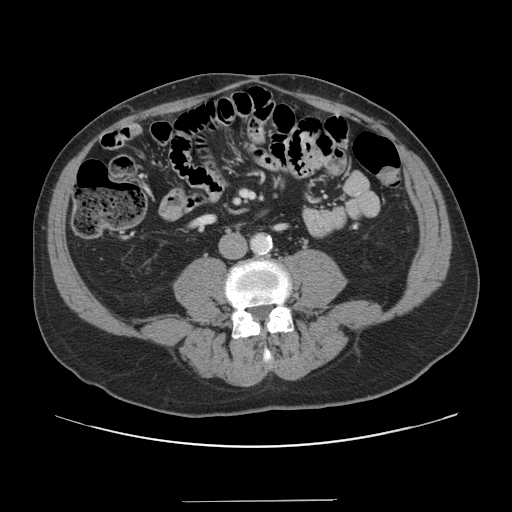
Contrast-enhanced abdominal CT, one axial slice. Slice 13 of 151 in the series (ordered by position). 120 kVp. Intravenous contrast given. Soft-tissue window (W 400 / L 40 HU). 2.5 mm slice thickness. 512 × 512 image matrix. Male patient, age 63 years. From the clinical record (not read from this slice): diagnosis: colorectal cancer liver metastases, imaged before liver resection; multiple liver metastases: no; largest metastasis: 2.1 cm; chemotherapy before resection: no.
Structures marked on this image (manually delineated by an expert):
- portal vein (with intrahepatic branches): box from (x=244, y=193) to (x=252, y=196) px